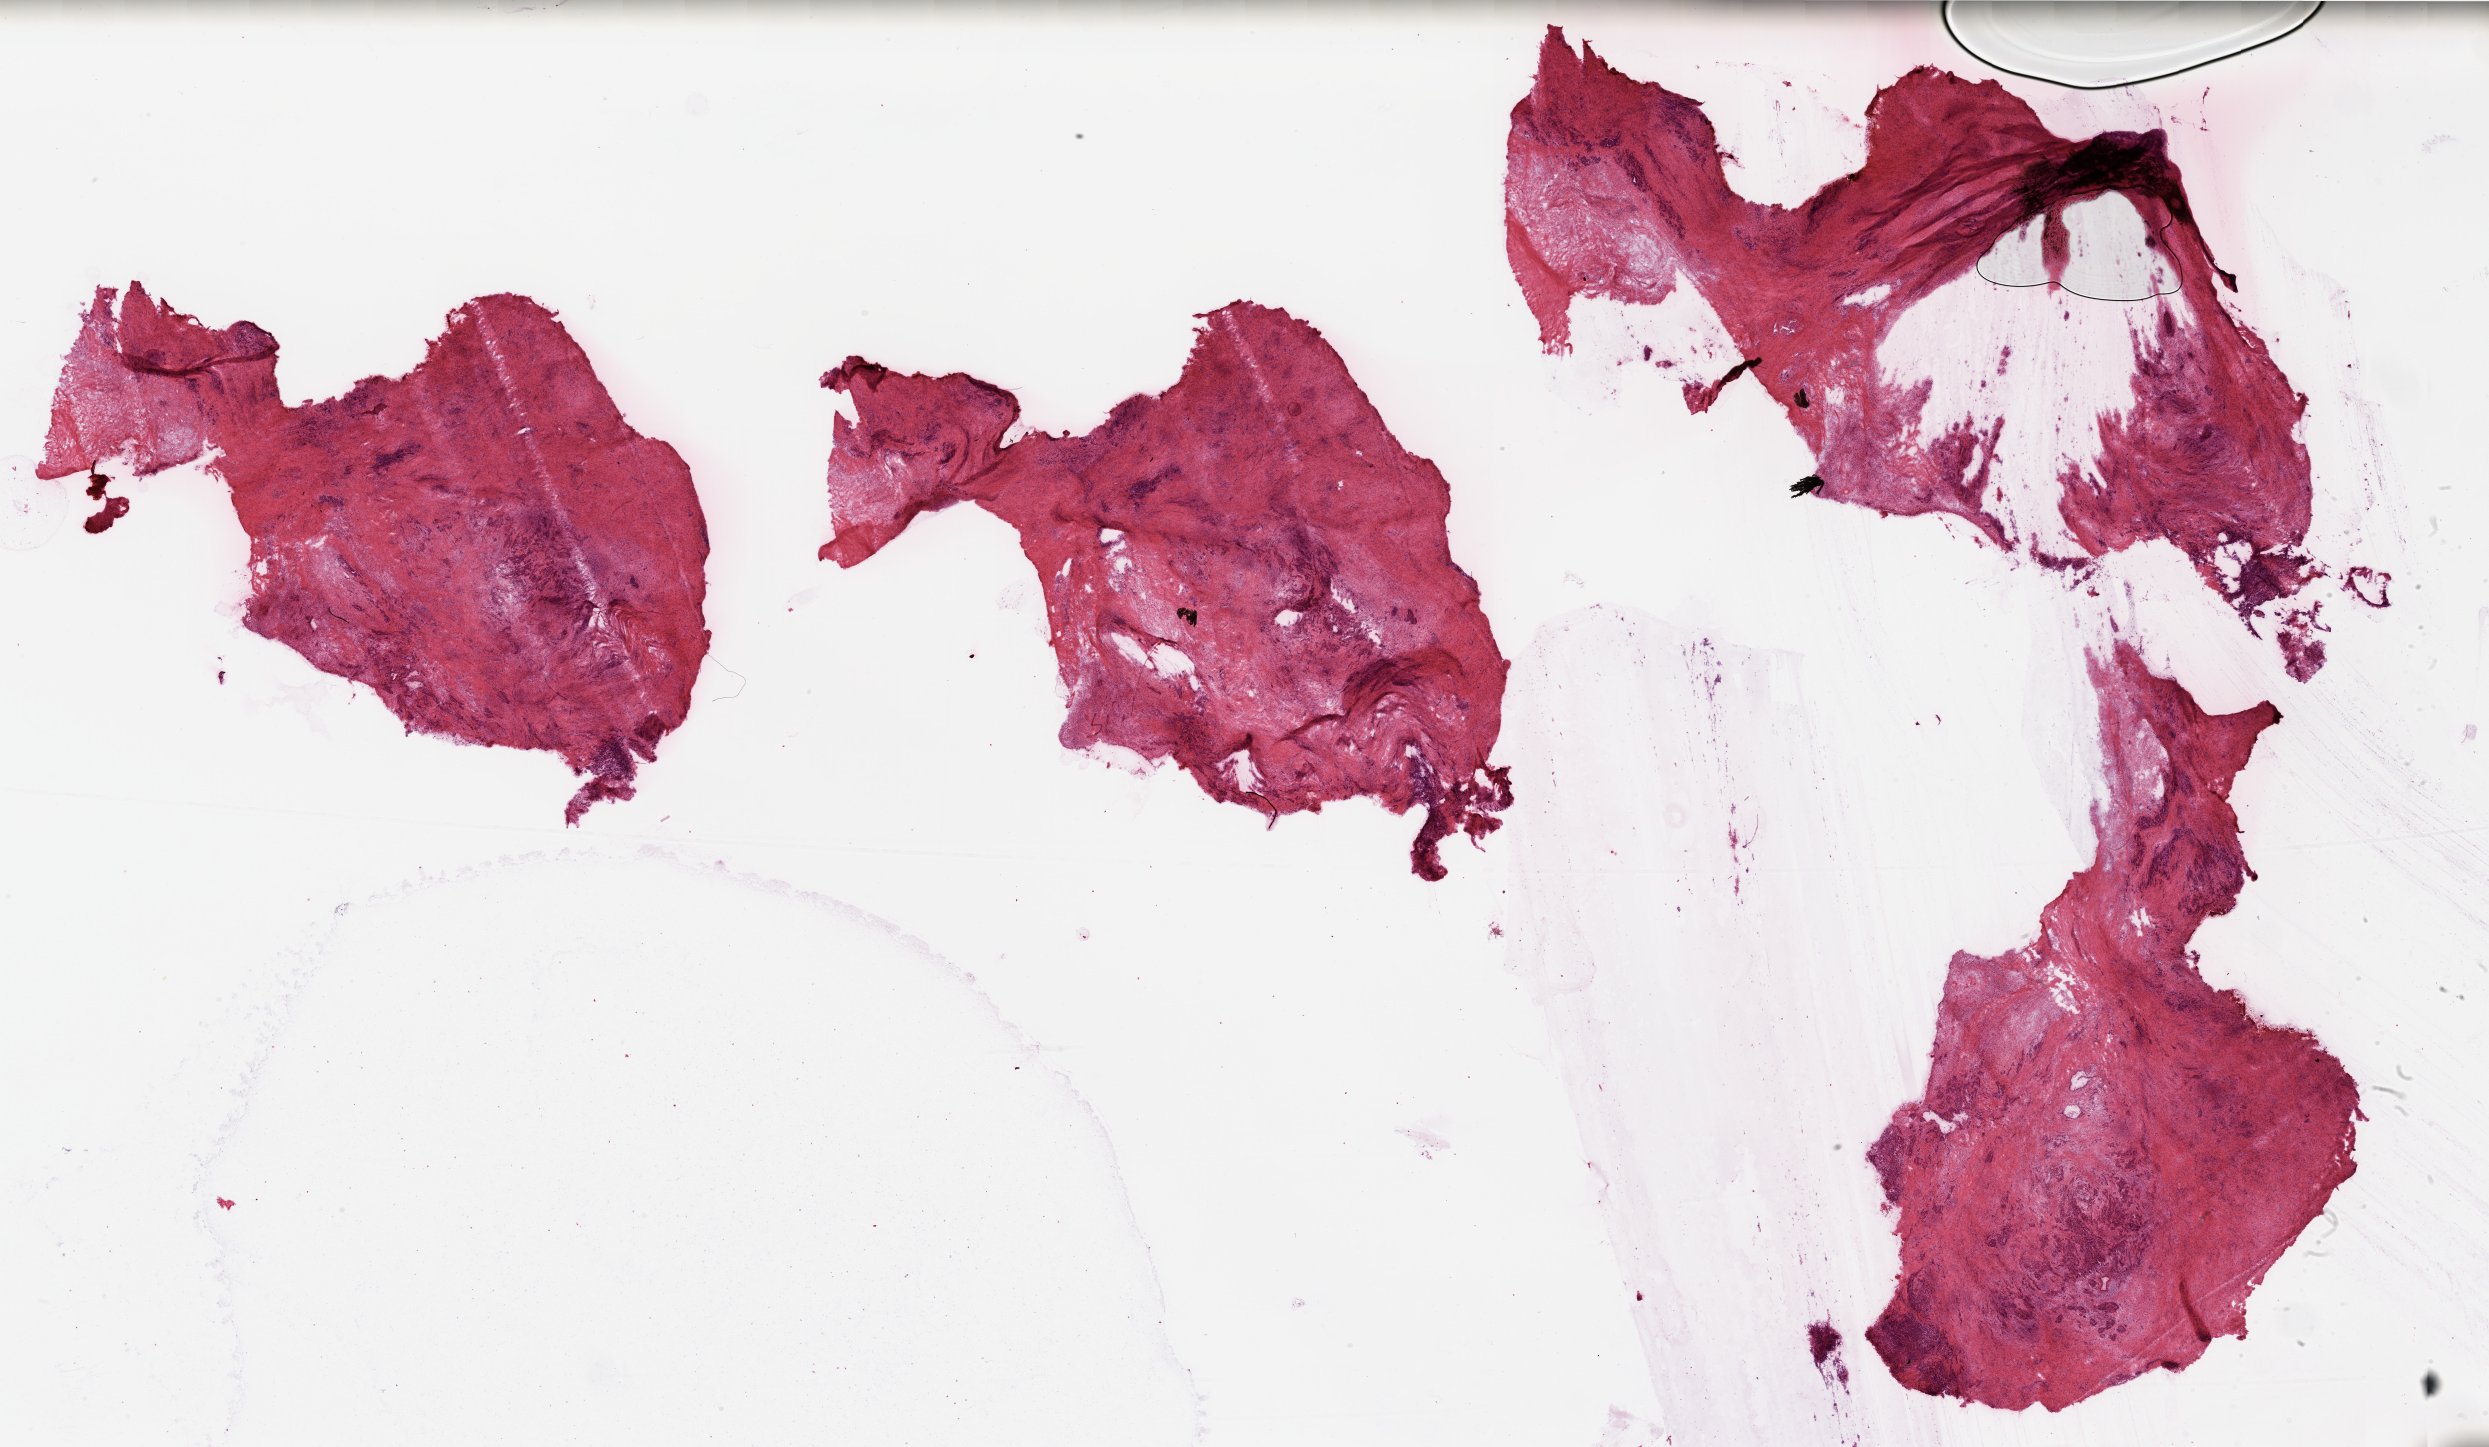
Digitized H&E tissue section (whole slide) — whole scanned area (about 39.4 x 22.9 mm, acquisition: 20x scan) shown as a low-resolution overview; tumour tissue sample, sampled site: pancreas. Patient: male, age 58 years. Histologic grade: G3 (poorly differentiated). Pathologist review of this section (percent, as recorded): tumour nuclei 20%, necrosis 0%.
AJCC pathologic stage: IV. Histologic diagnosis: Infiltrating duct carcinoma, NOS. Primary tumour site (as recorded): head.